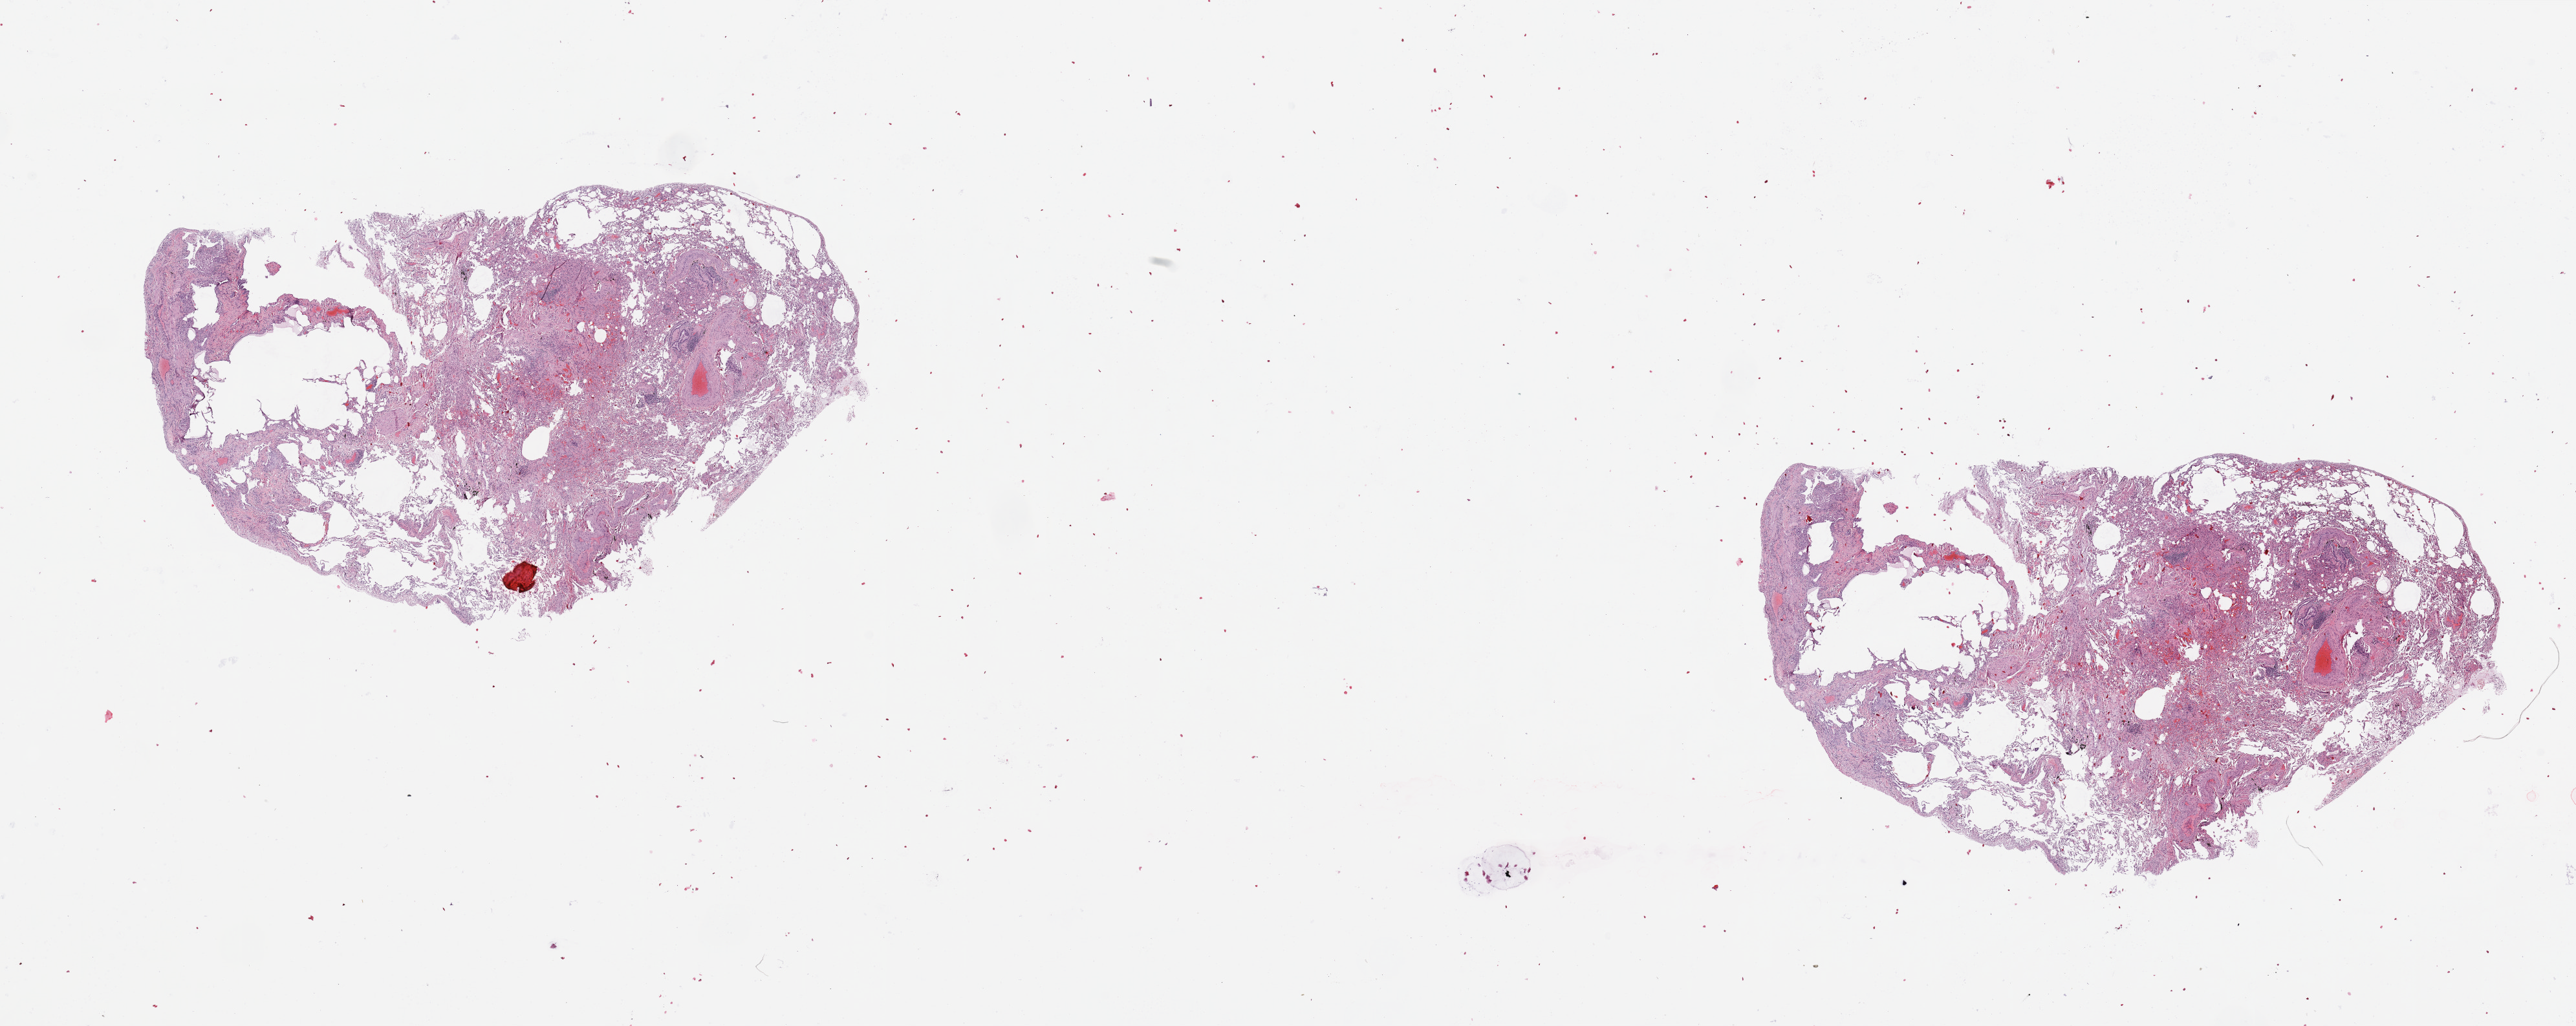
Digitized H&E-stained tissue section (whole slide), shown as a low-resolution overview of the whole scanned area (about 31.5 x 12.6 mm, from a 20x scan). Normal (non-tumour) tissue sample, lung. Patient: male, age 62 years.
This section: normal (non-tumour) tissue from the same patient. Patient diagnosis: Squamous cell carcinoma, NOS.